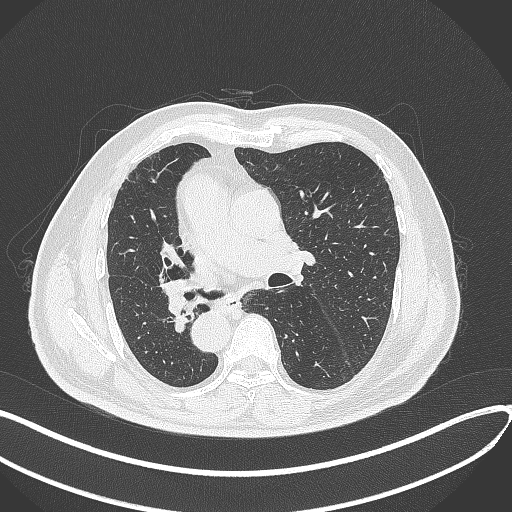
Chest CT, one axial slice. Slice 157 of 300 in the series (ordered by position). Reconstruction kernel B70f. Lung window (W 1500 / L -600 HU). 512 × 512 image matrix. Male patient, age 67 years. From the clinical record (not read from this slice): clinical TNM (as recorded): T2a N0 M0.
Outlined on this slice (bounding box drawn by a radiologist):
- lung tumour (recorded histology: squamous cell carcinoma): bounding box (x1, y1, x2, y2) in pixels: (158, 278, 195, 320)